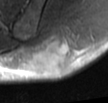
MRI of an extremity soft-tissue mass, one axial slice. Position 16 of 42 along the scan axis. T2-weighted fat-saturated. MR volume resampled by the dataset authors to the PET/CT grid (not the native acquisition matrix). 3.27 mm slice thickness. 108 × 103 image matrix, field of view 105 × 101 mm. Male patient. From the clinical record (not read from this slice): histological type: leiomyosarcoma; grade: intermediate; site of the primary tumour: left pelvis.
Outlined on this slice (expert contour drawn on MRI and transferred to this co-registered scan by the dataset authors):
- gross tumour volume (mass): box from (x=30, y=37) to (x=72, y=77) px